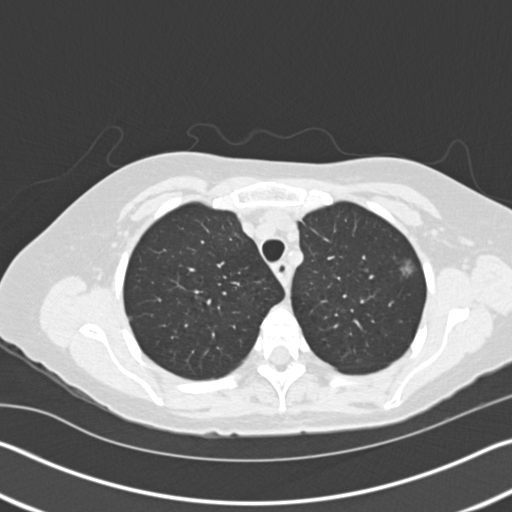
Low-dose screening chest CT, axial slice, baseline screening round, lung window (W 1500 / L -600 HU), 2 mm slice thickness, slice 35 of 154 in the series, 512 × 512 image matrix. Female participant, aged 60 years at enrolment. Former smoker at enrolment.
• Expert reader's lesion annotation, bounding box <388,249,442,292> (left, top, right, bottom; pixels).
• The screening reader recorded 2 non-calcified nodules or masses ≥4 mm on this exam (right lower lobe, left upper lobe); which of them this box marks is not recorded.
• Official screen result: positive, change unspecified: nodule(s) >= 4 mm or enlarging nodule(s), mass(es), or other non-specific abnormalities suspicious for lung cancer.